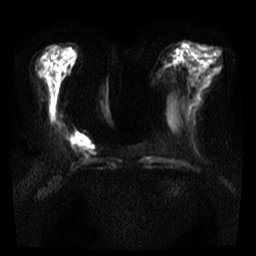
Breast MRI, one axial slice; diffusion-weighted series; image 2 of 4 stored at this slice position (different b-values; order by instance number); 3 T; 5 mm slice thickness; 256 × 256 image matrix, field of view 300 × 300 mm. Female patient.
Structures marked on this image (manually delineated by an expert):
- tumour on diffusion-weighted imaging: box from (x=68, y=131) to (x=92, y=149) px